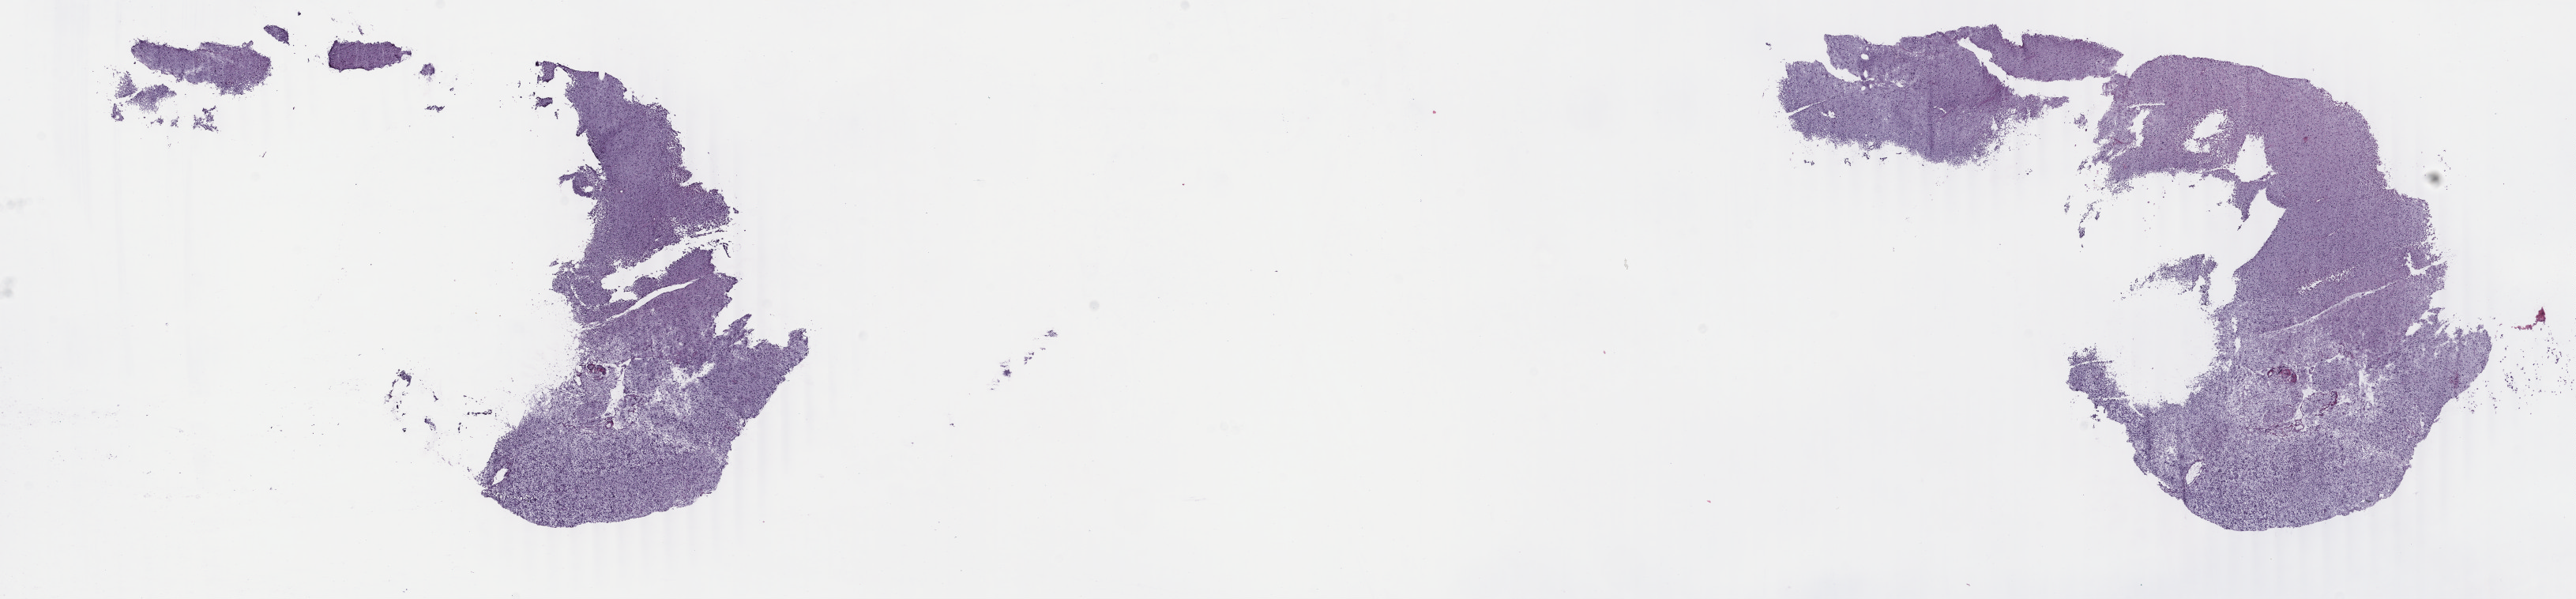
H&E-stained whole-slide image — low-resolution overview of the scanned area, about 25.9 x 6.0 mm, frozen section from the top of the tissue portion, primary tumour sample from the brain. Female, age 55 years at initial diagnosis. Histologic grade: G3 (poorly differentiated). Composition of this section per pathologist review: tumour cells 60%, tumour nuclei 90%, normal cells 40%, stromal cells 0%, necrosis 0%. Inflammatory infiltration, as recorded: lymphocyte infiltration 0%, monocyte infiltration 0%, neutrophil infiltration 0%.
- diagnosis: Astrocytoma, anaplastic